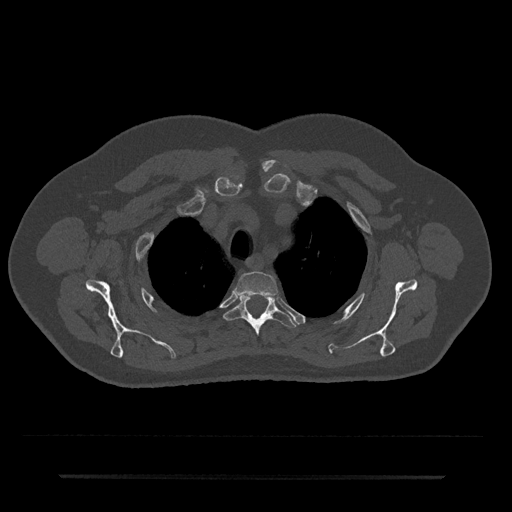
CT including the spine, one axial slice; position 578 of 797 along the scan axis; 120 kVp; bone window (W 1800 / L 400 HU); 0.5 mm slice thickness; 512 × 512 image matrix, field of view 437 × 437 mm. Patient: male, 69 years. From the clinical record (not read from this slice): primary cancer: prostate.
Annotated regions visible in this slice (semi-automatic segmentation, software-assisted and operator-edited):
- T2 vertebra: bounding box [x1, y1, x2, y2] px = [235, 272, 278, 295]
- T3 vertebra: [224, 295, 297, 335]